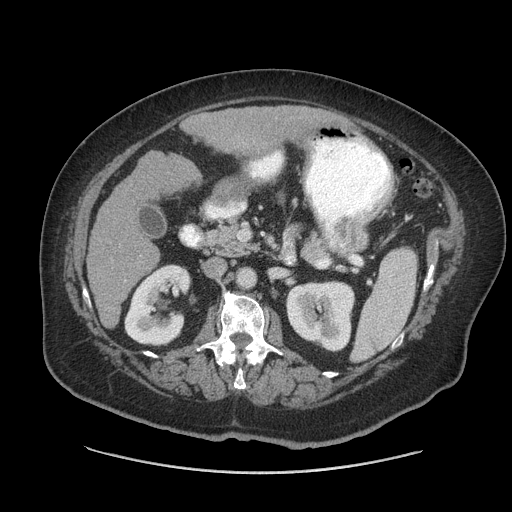
Contrast-enhanced abdominal CT (liver protocol), one axial slice. Slice 27 of 91 in the series (ordered by position). 140 kVp. Soft-tissue window (W 400 / L 40 HU). 2.5 mm slice thickness. 512 × 512 image matrix. From the clinical record (not read from this slice): diagnosis: hepatocellular carcinoma (patient treated with transarterial chemoembolisation; whether this scan precedes or follows treatment is not stated here); TNM stage (as recorded): Stage-I; Child-Pugh class: A.
Structures marked on this image (semi-automatic segmentation, software-assisted and operator-edited):
- liver parenchyma outside the tumour (the mass and vessels are separate outlines, so this box may not span the whole liver): bounding box [x1, y1, x2, y2] px = [86, 106, 320, 326]